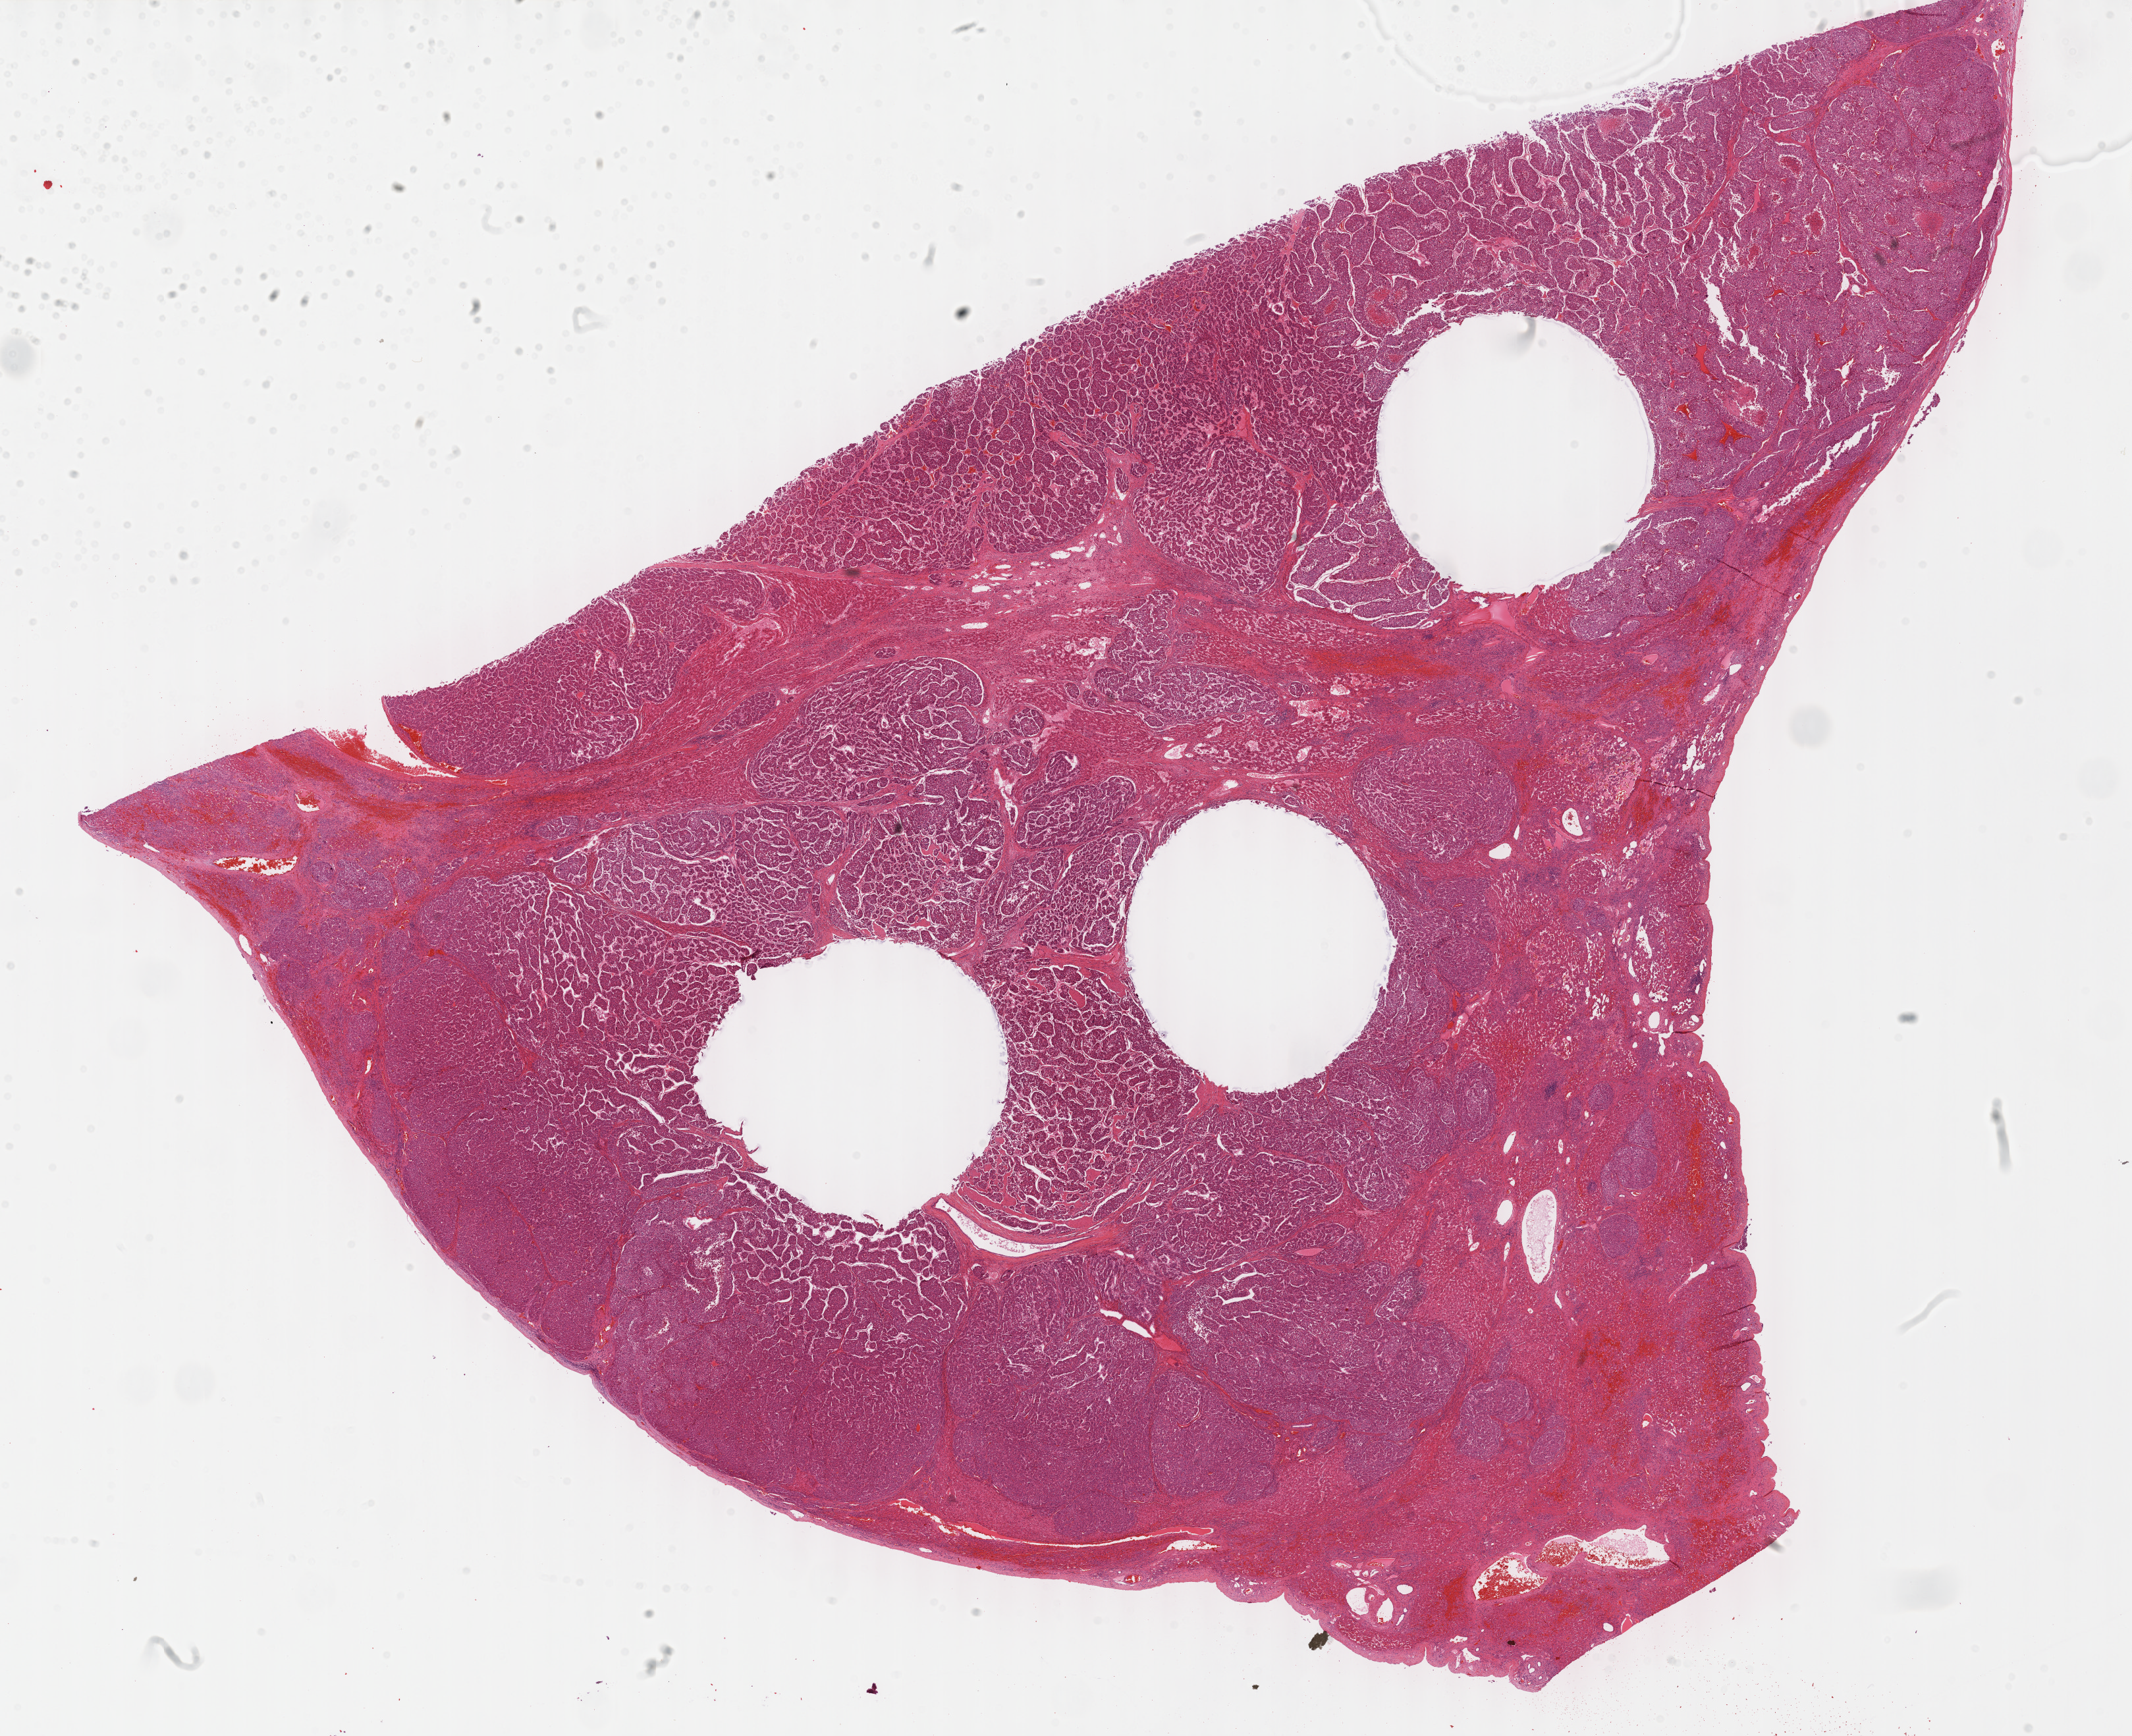
H&E whole-slide image — low-resolution overview of the scanned area, about 26.2 x 21.3 mm. Formalin-fixed paraffin-embedded (FFPE) diagnostic section. Primary tumour sample from the liver. Male, age 69 years at initial diagnosis. Histologic grade: G3 (poorly differentiated).
AJCC pathologic stage: II. Pathologic diagnosis: Hepatocellular carcinoma, NOS.